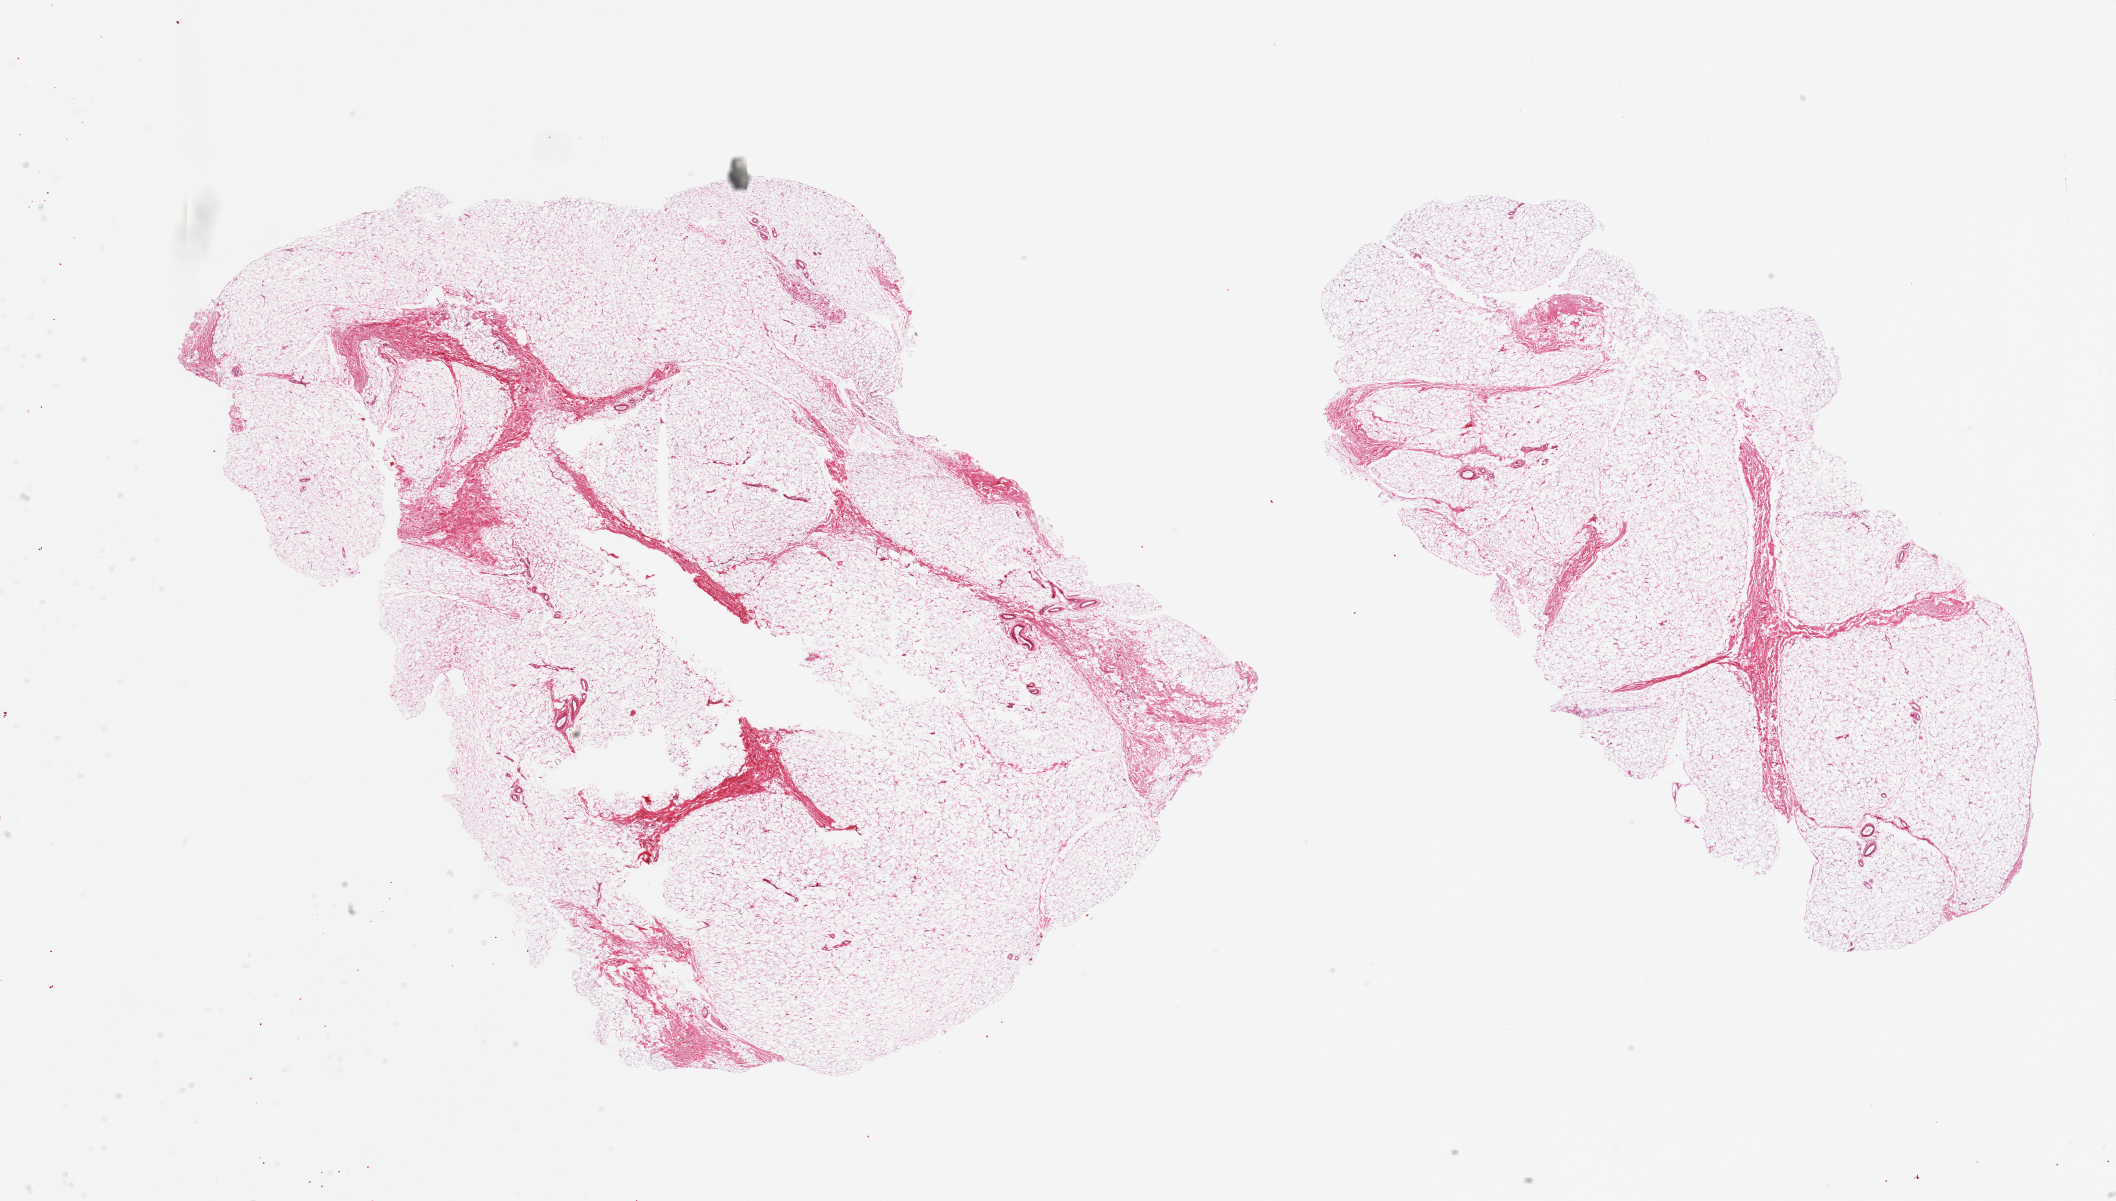
Haematoxylin and eosin whole-slide image, low-resolution overview of the scanned area, about 33.5 x 19.0 mm (slide scanned at 20x); PAXgene-fixed, paraffin-embedded tissue; target tissue: breast; donor tissue sample. Male donor.
Pathologist's review note for this sample: 2 pieces; mature adipose tissue and ~15% fibrovascular component; no evidence of ductal structures.